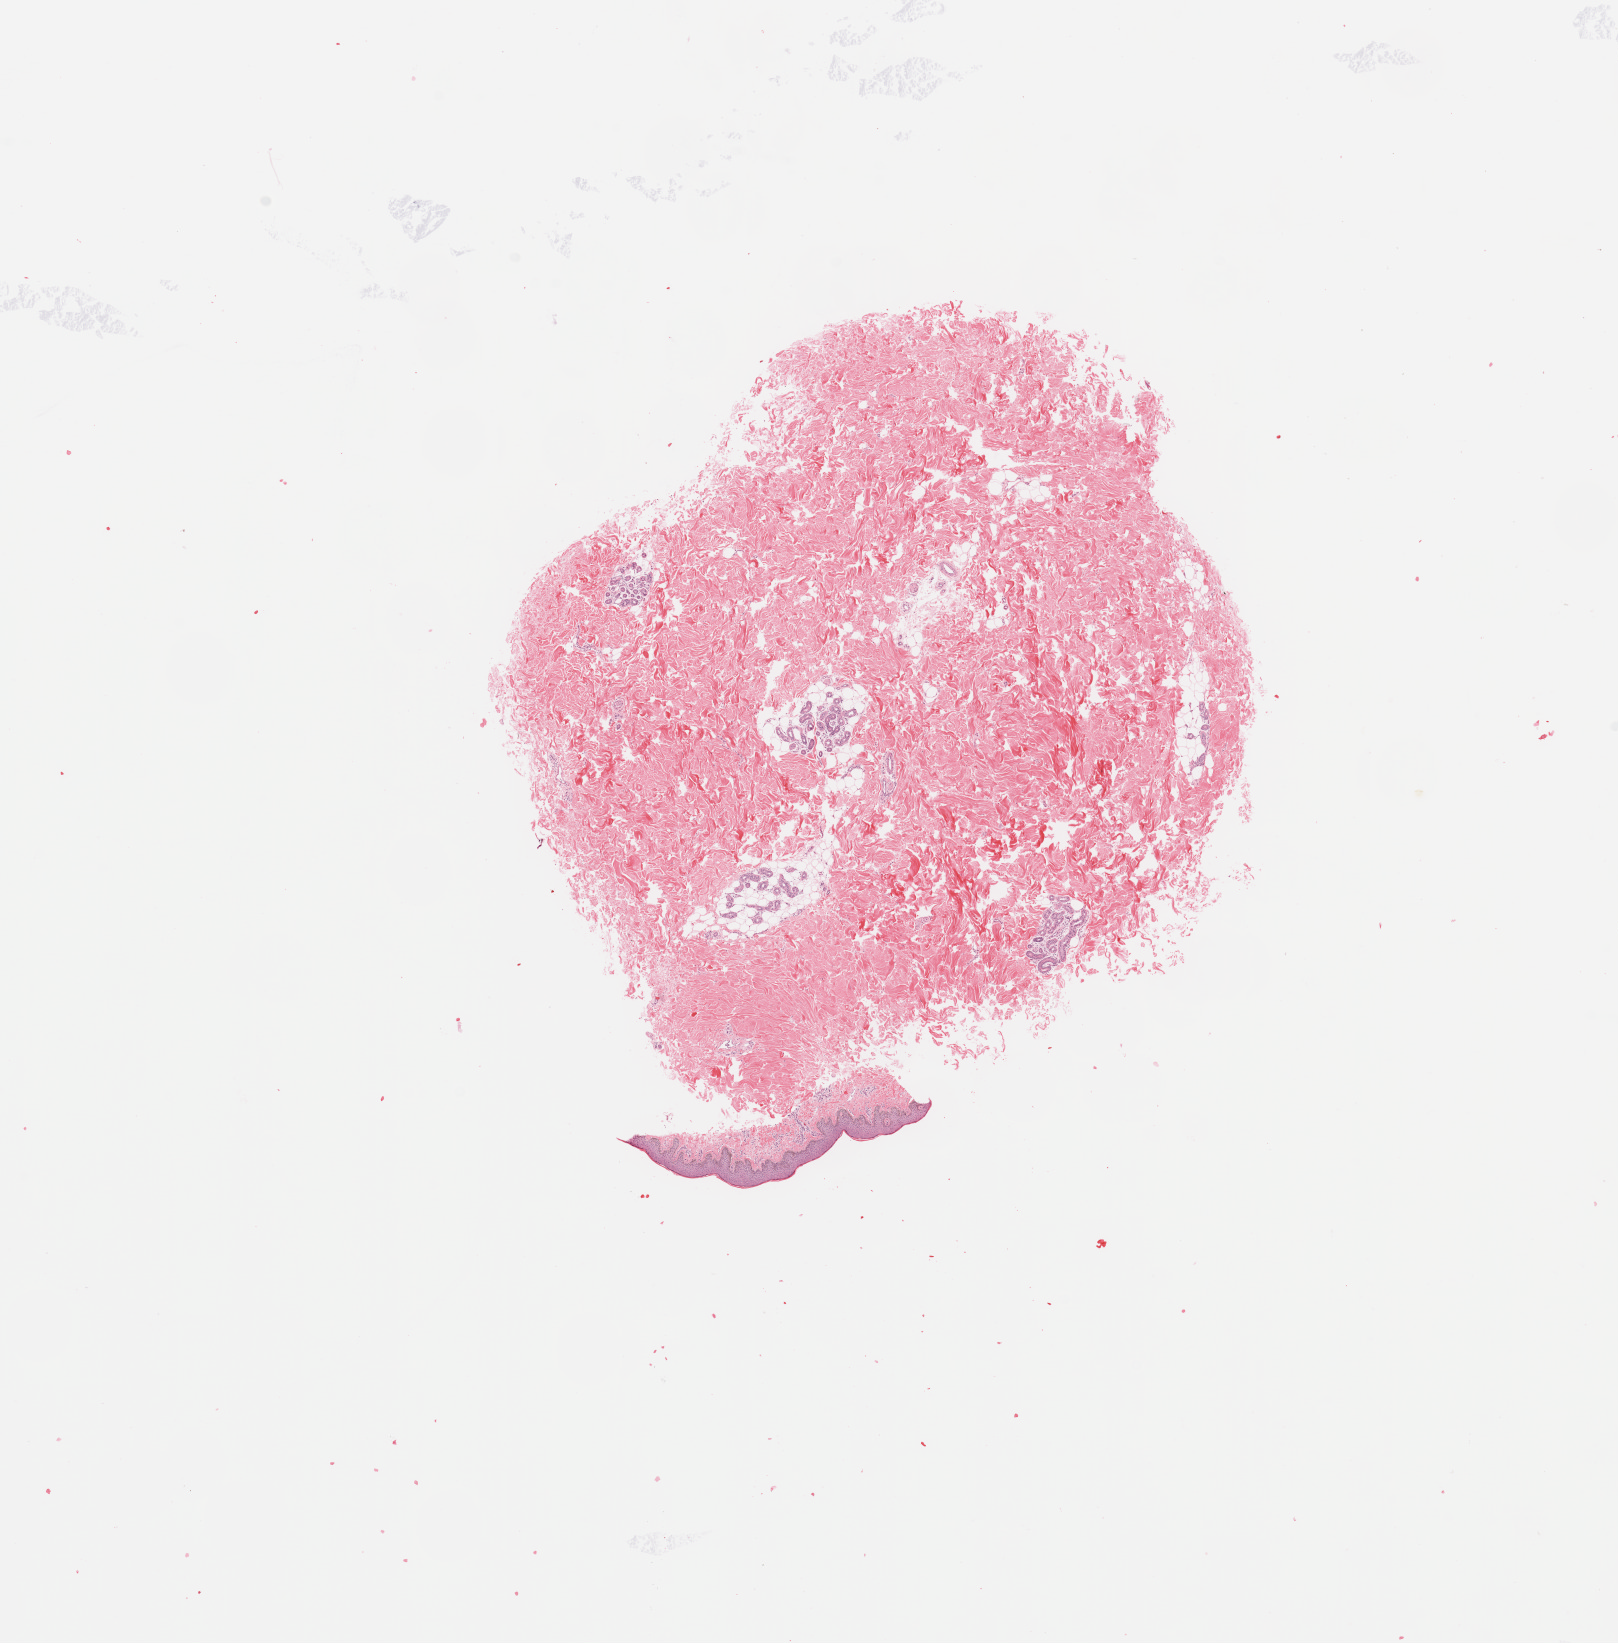
Hematoxylin and eosin (H&E) stained whole-slide image — shown as a low-resolution overview of the whole scanned area (about 12.8 x 13.0 mm, from a 20x scan), normal (non-tumour) tissue (melanoma cohort); sampled site not recorded. Patient: female, age 45 years.
This section: normal (non-tumour) tissue from the same patient. Patient diagnosis (cohort enrolment): cutaneous melanoma (skin).